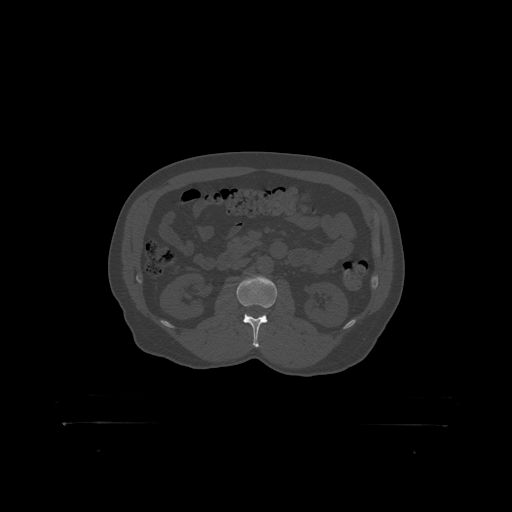
CT including the spine, one axial slice. Slice 290 of 399 in the series (ordered by position). Reconstruction kernel STANDARD. Bone window (W 1800 / L 400 HU). 512 × 512 image matrix, field of view 650 × 650 mm. Male patient, age 46 years. From the clinical record (not read from this slice): primary cancer: skin.
Outlined on this slice (semi-automatic segmentation, software-assisted and operator-edited):
- L2 vertebra: bounding box [x1, y1, x2, y2] px = [237, 276, 278, 319]